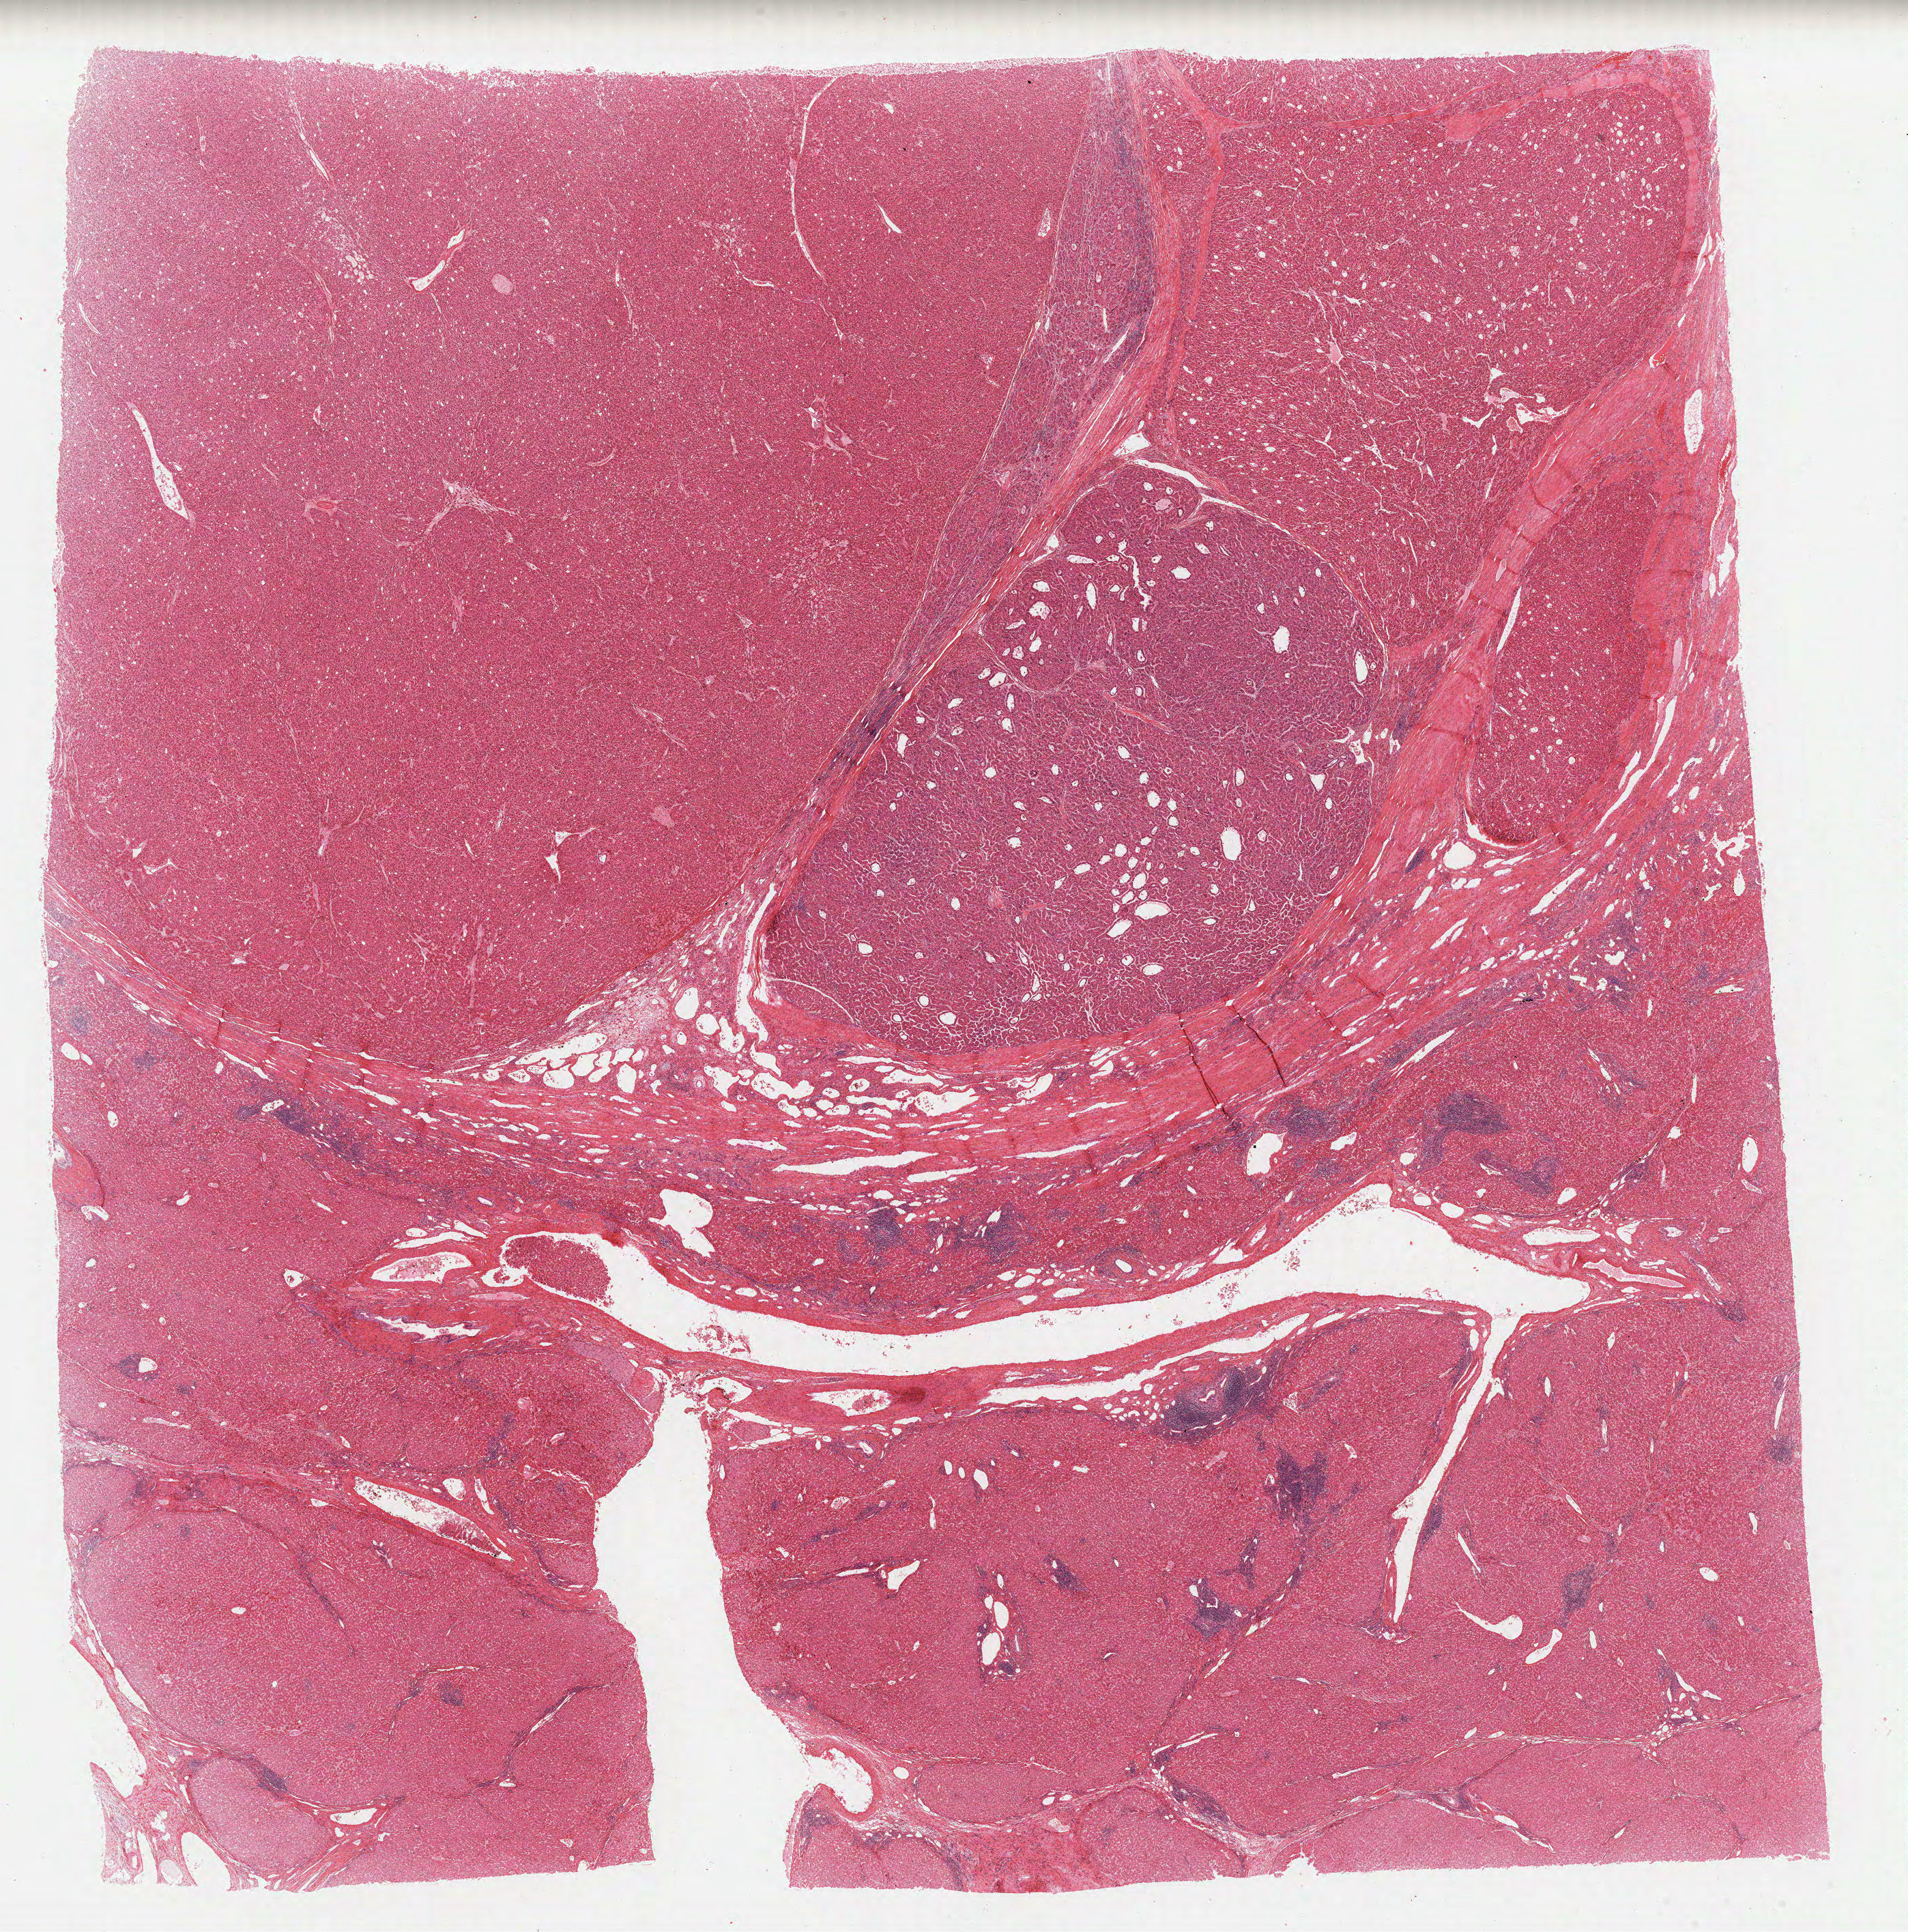
Digitized H&E tissue section (whole slide), low-resolution overview of the scanned area, about 22.1 x 22.4 mm, formalin-fixed paraffin-embedded (FFPE) diagnostic section, sample: primary tumour, liver. Male patient; age at initial diagnosis 55 years. Histologic grade: G2 (moderately differentiated).
Diagnosis: Hepatocellular carcinoma, NOS. AJCC pathologic stage: IIIA (6th edition).